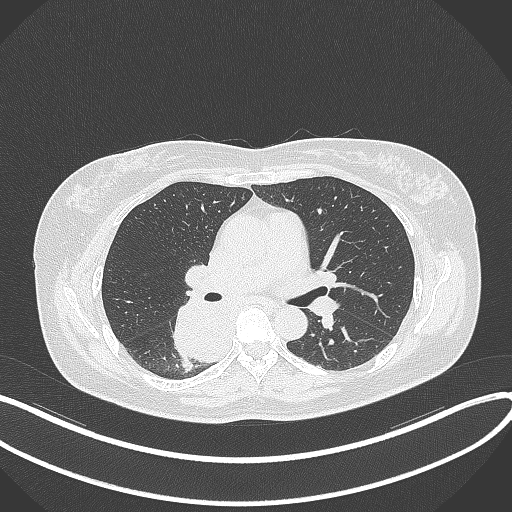
Chest CT, one axial slice; slice 209 of 331 in the series (ordered by position); reconstruction kernel B70f; lung window (W 1500 / L -600 HU); 1 mm slice thickness; 512 × 512 image matrix. Female patient, age 54 years. From the clinical record (not read from this slice): clinical TNM (as recorded): T4 N0 M0.
Outlined on this slice (rectangle marked by the reading radiologist):
- lung tumour (recorded histology: adenocarcinoma): bounding box <165,299,233,368> (left, top, right, bottom; pixels)